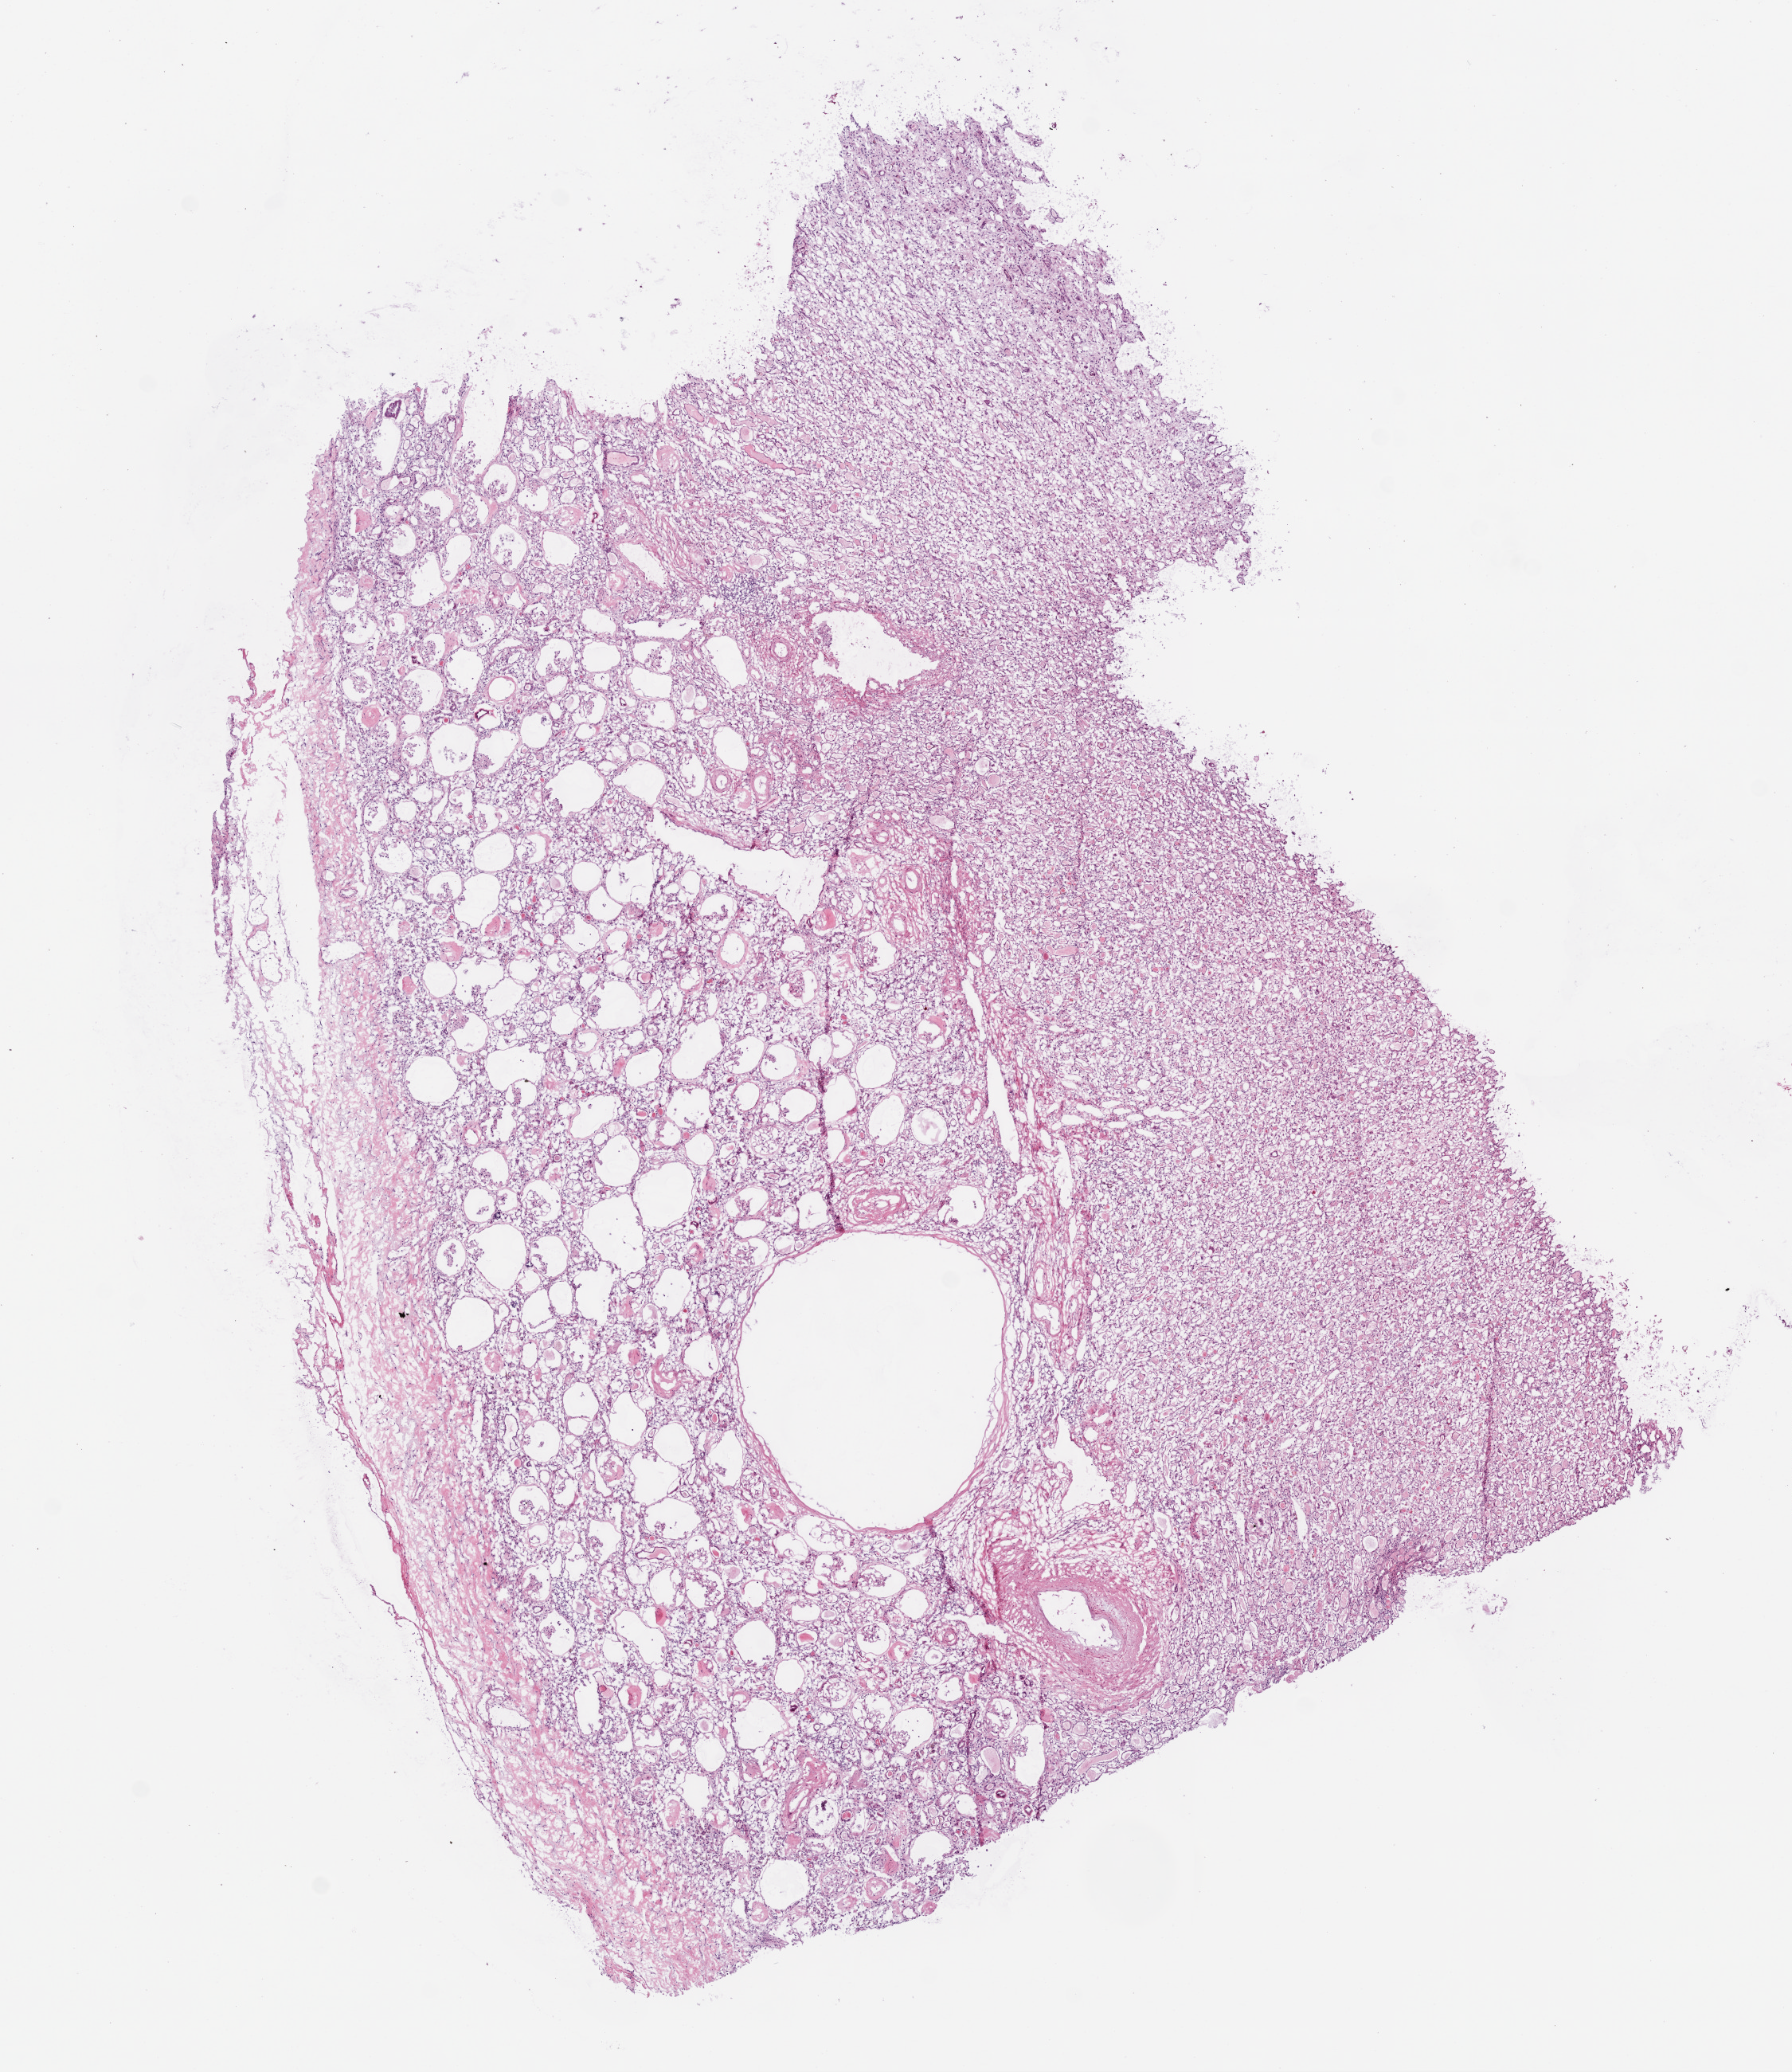
Digitized Hematoxylin and eosin (H&E) stained tissue section (whole slide) — low-resolution overview of the scanned area, about 9.0 x 10.4 mm (slide scanned at 20x). Frozen section. Solid tissue normal (non-tumour tissue) sample from the kidney. Female patient; age at initial diagnosis 53 years.
This section: solid tissue normal (non-tumour) sample from the same patient. Patient diagnosis: Clear cell adenocarcinoma, NOS.